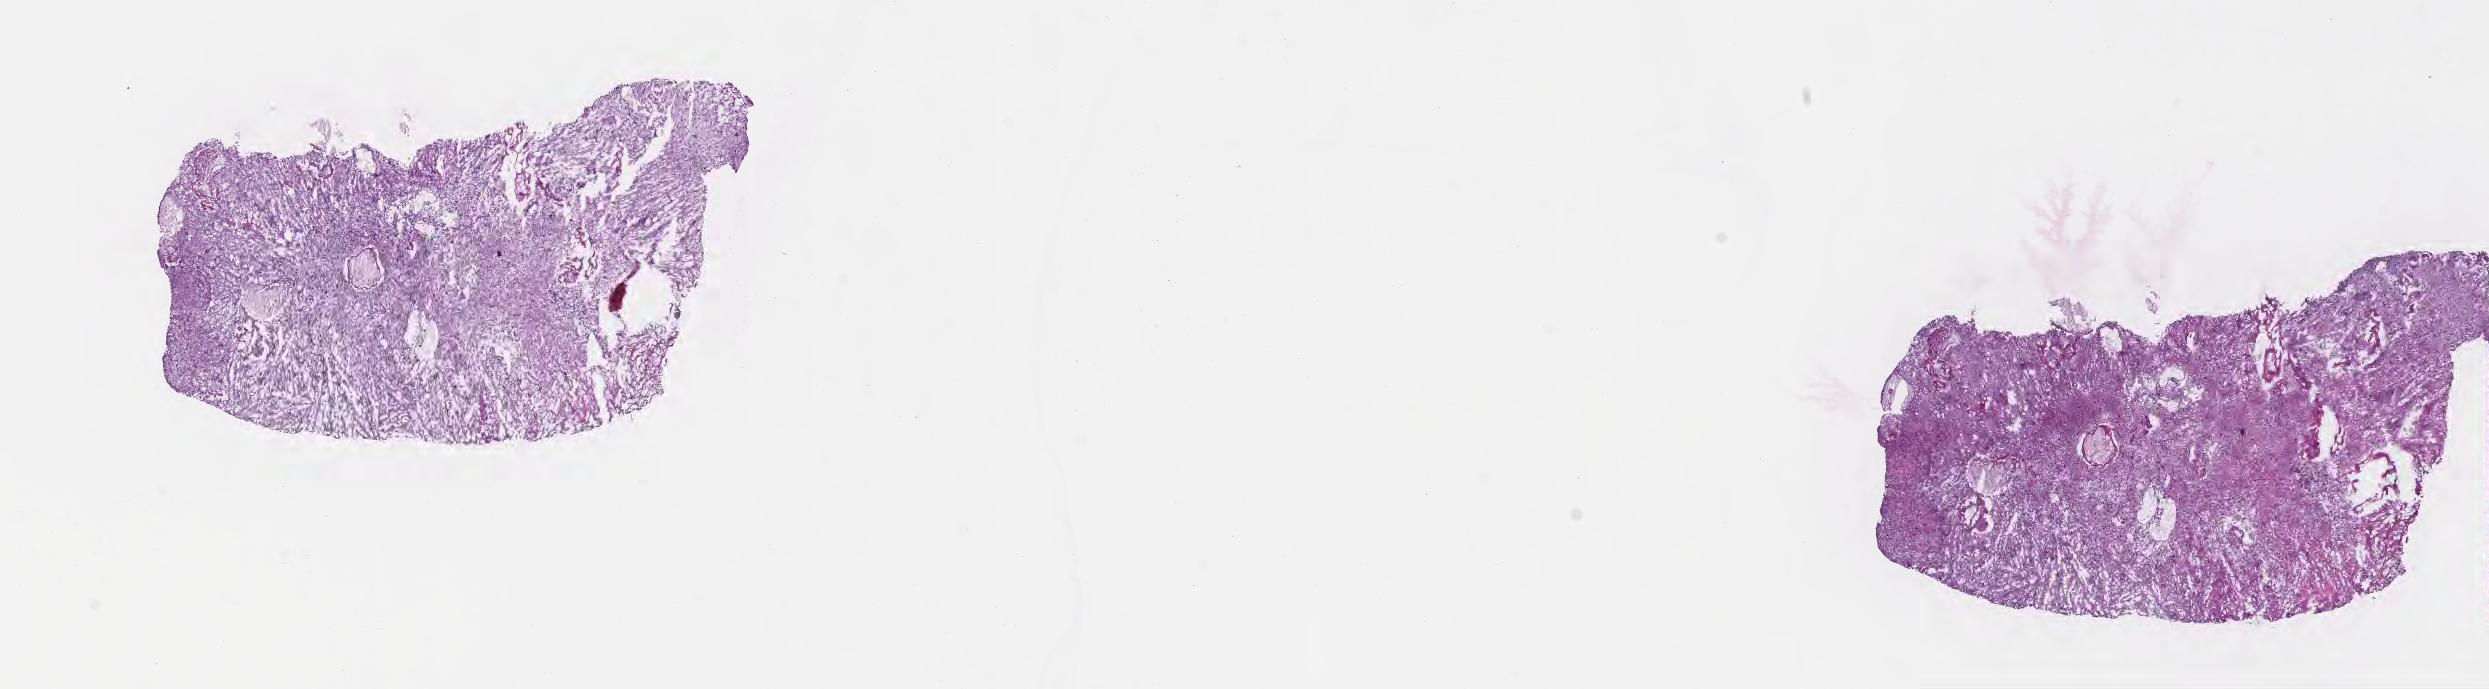
Digitized H&E-stained section, low-resolution overview of the scanned area, about 20.1 x 5.6 mm, frozen section, specimen: recurrent tumor, site: brain. Male patient; age at initial diagnosis 48 years. Composition of this section per pathologist review: tumor cells 56%, tumor nuclei 88%.
Patient diagnosis: Glioblastoma, NOS.